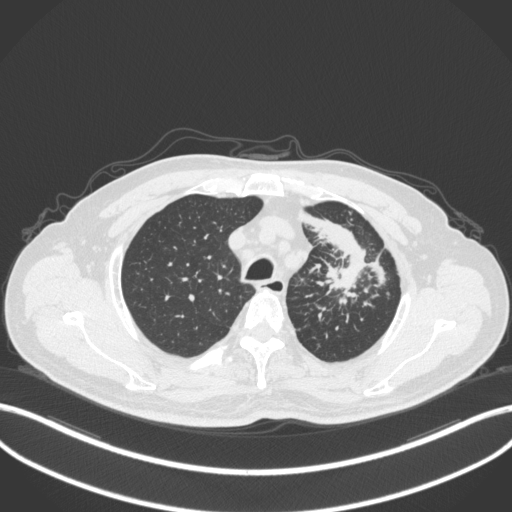
Chest CT, one axial slice. Slice 286 of 386 in the series (ordered by position). Reconstruction kernel B31f. 120 kVp. Lung window (W 1500 / L -600 HU). 512 × 512 image matrix. Male patient, age 69 years. Case-level facts recorded for this patient, not image findings: clinical TNM (as recorded): T2a N2 M0.
Structures marked on this image (bounding box drawn by a radiologist):
- lung tumour (recorded histology: adenocarcinoma): box from (x=301, y=210) to (x=373, y=299) px